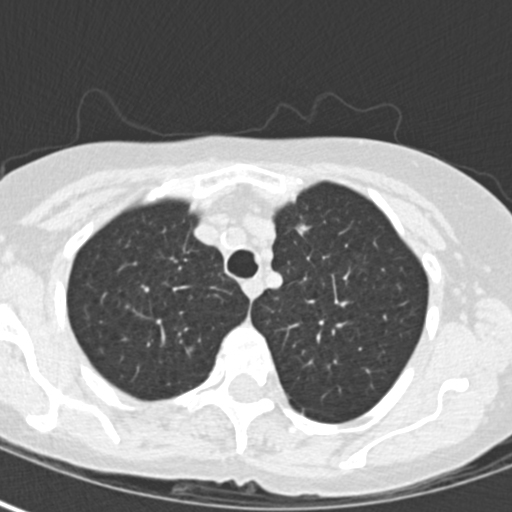
Low-dose screening chest CT, one axial slice. Position 126 of 163 along the scan axis. 120 kVp. Lung window (W 1500 / L -600 HU). 2 mm slice thickness. 512 × 512 image matrix, field of view 280 × 280 mm.
Annotated regions visible in this slice (outlined manually by an expert reader):
- lesion 1 (tumor, upper lobe of left lung): bounding box <296,225,310,236> (left, top, right, bottom; pixels)